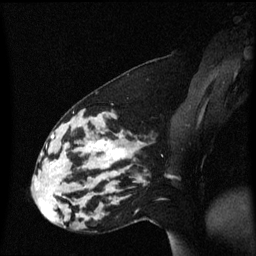
Breast MRI (dynamic contrast-enhanced), one sagittal slice. Position 22 of 60 along the scan axis. Dynamic contrast-enhanced series, image 2 of 3 at this slice position (ordered by acquisition). 1.5 T. TE 4.2 ms, TR 8.4 ms. 2 mm slice thickness. 256 × 256 image matrix. Female patient, age 33 years. Case-level facts recorded for this patient, not image findings: setting: breast cancer imaged before/during neoadjuvant chemotherapy; receptor status: triple-negative.
Annotated regions visible in this slice (semi-automatic segmentation, software-assisted and operator-edited):
- analysis volume of interest (the breast-tissue region the enhancement analysis was run in; not a lesion): bounding box <44,123,139,189> (left, top, right, bottom; pixels)
- tumour enhancement mask (voxels above the 70 % enhancement threshold inside the analysis volume of interest): <89,141,129,164>